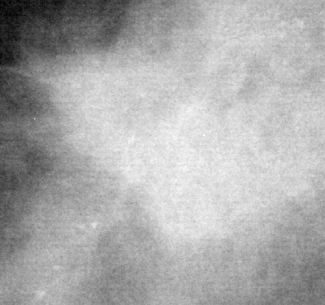
Crop from a digitized film mammogram around one marked abnormality, right breast, CC view, BI-RADS breast density category 3 (scale 1–4).
- Mass, shape irregular, margins ill defined / spiculated; BI-RADS assessment category 4; pathology (as recorded): malignant.